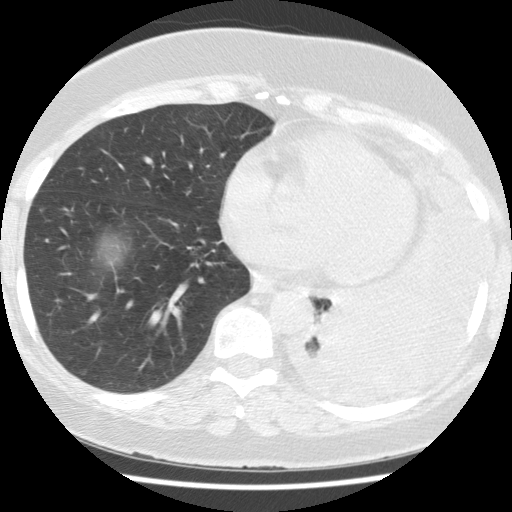
Axial slice from a low-dose chest CT screening exam, first (baseline) screen, lung window (W 1500 / L -600 HU), 2.5 mm slice thickness, standard (soft-tissue) reconstruction kernel (STANDARD), slice 72 of 114 in the series, 512 × 512 image matrix. Female, age 65 years at enrolment. Current smoker at enrolment.
Expert-annotated lung lesion, box from (x=315, y=281) to (x=442, y=389) px. Screening reader's record for this exam (one nodule recorded; not confirmed to be the boxed lesion): non-calcified nodule or mass ≥4 mm, left lower lobe, 74 × 48 mm, spiculated (stellate) margins, soft tissue attenuation. Official screen result: positive, change unspecified: nodule(s) >= 4 mm or enlarging nodule(s), mass(es), or other non-specific abnormalities suspicious for lung cancer. Lung cancer was diagnosed 13 days after this screen: adenocarcinoma, NOS, left lower lobe, stage IV (AJCC 6th edition), 74 mm at pathology.